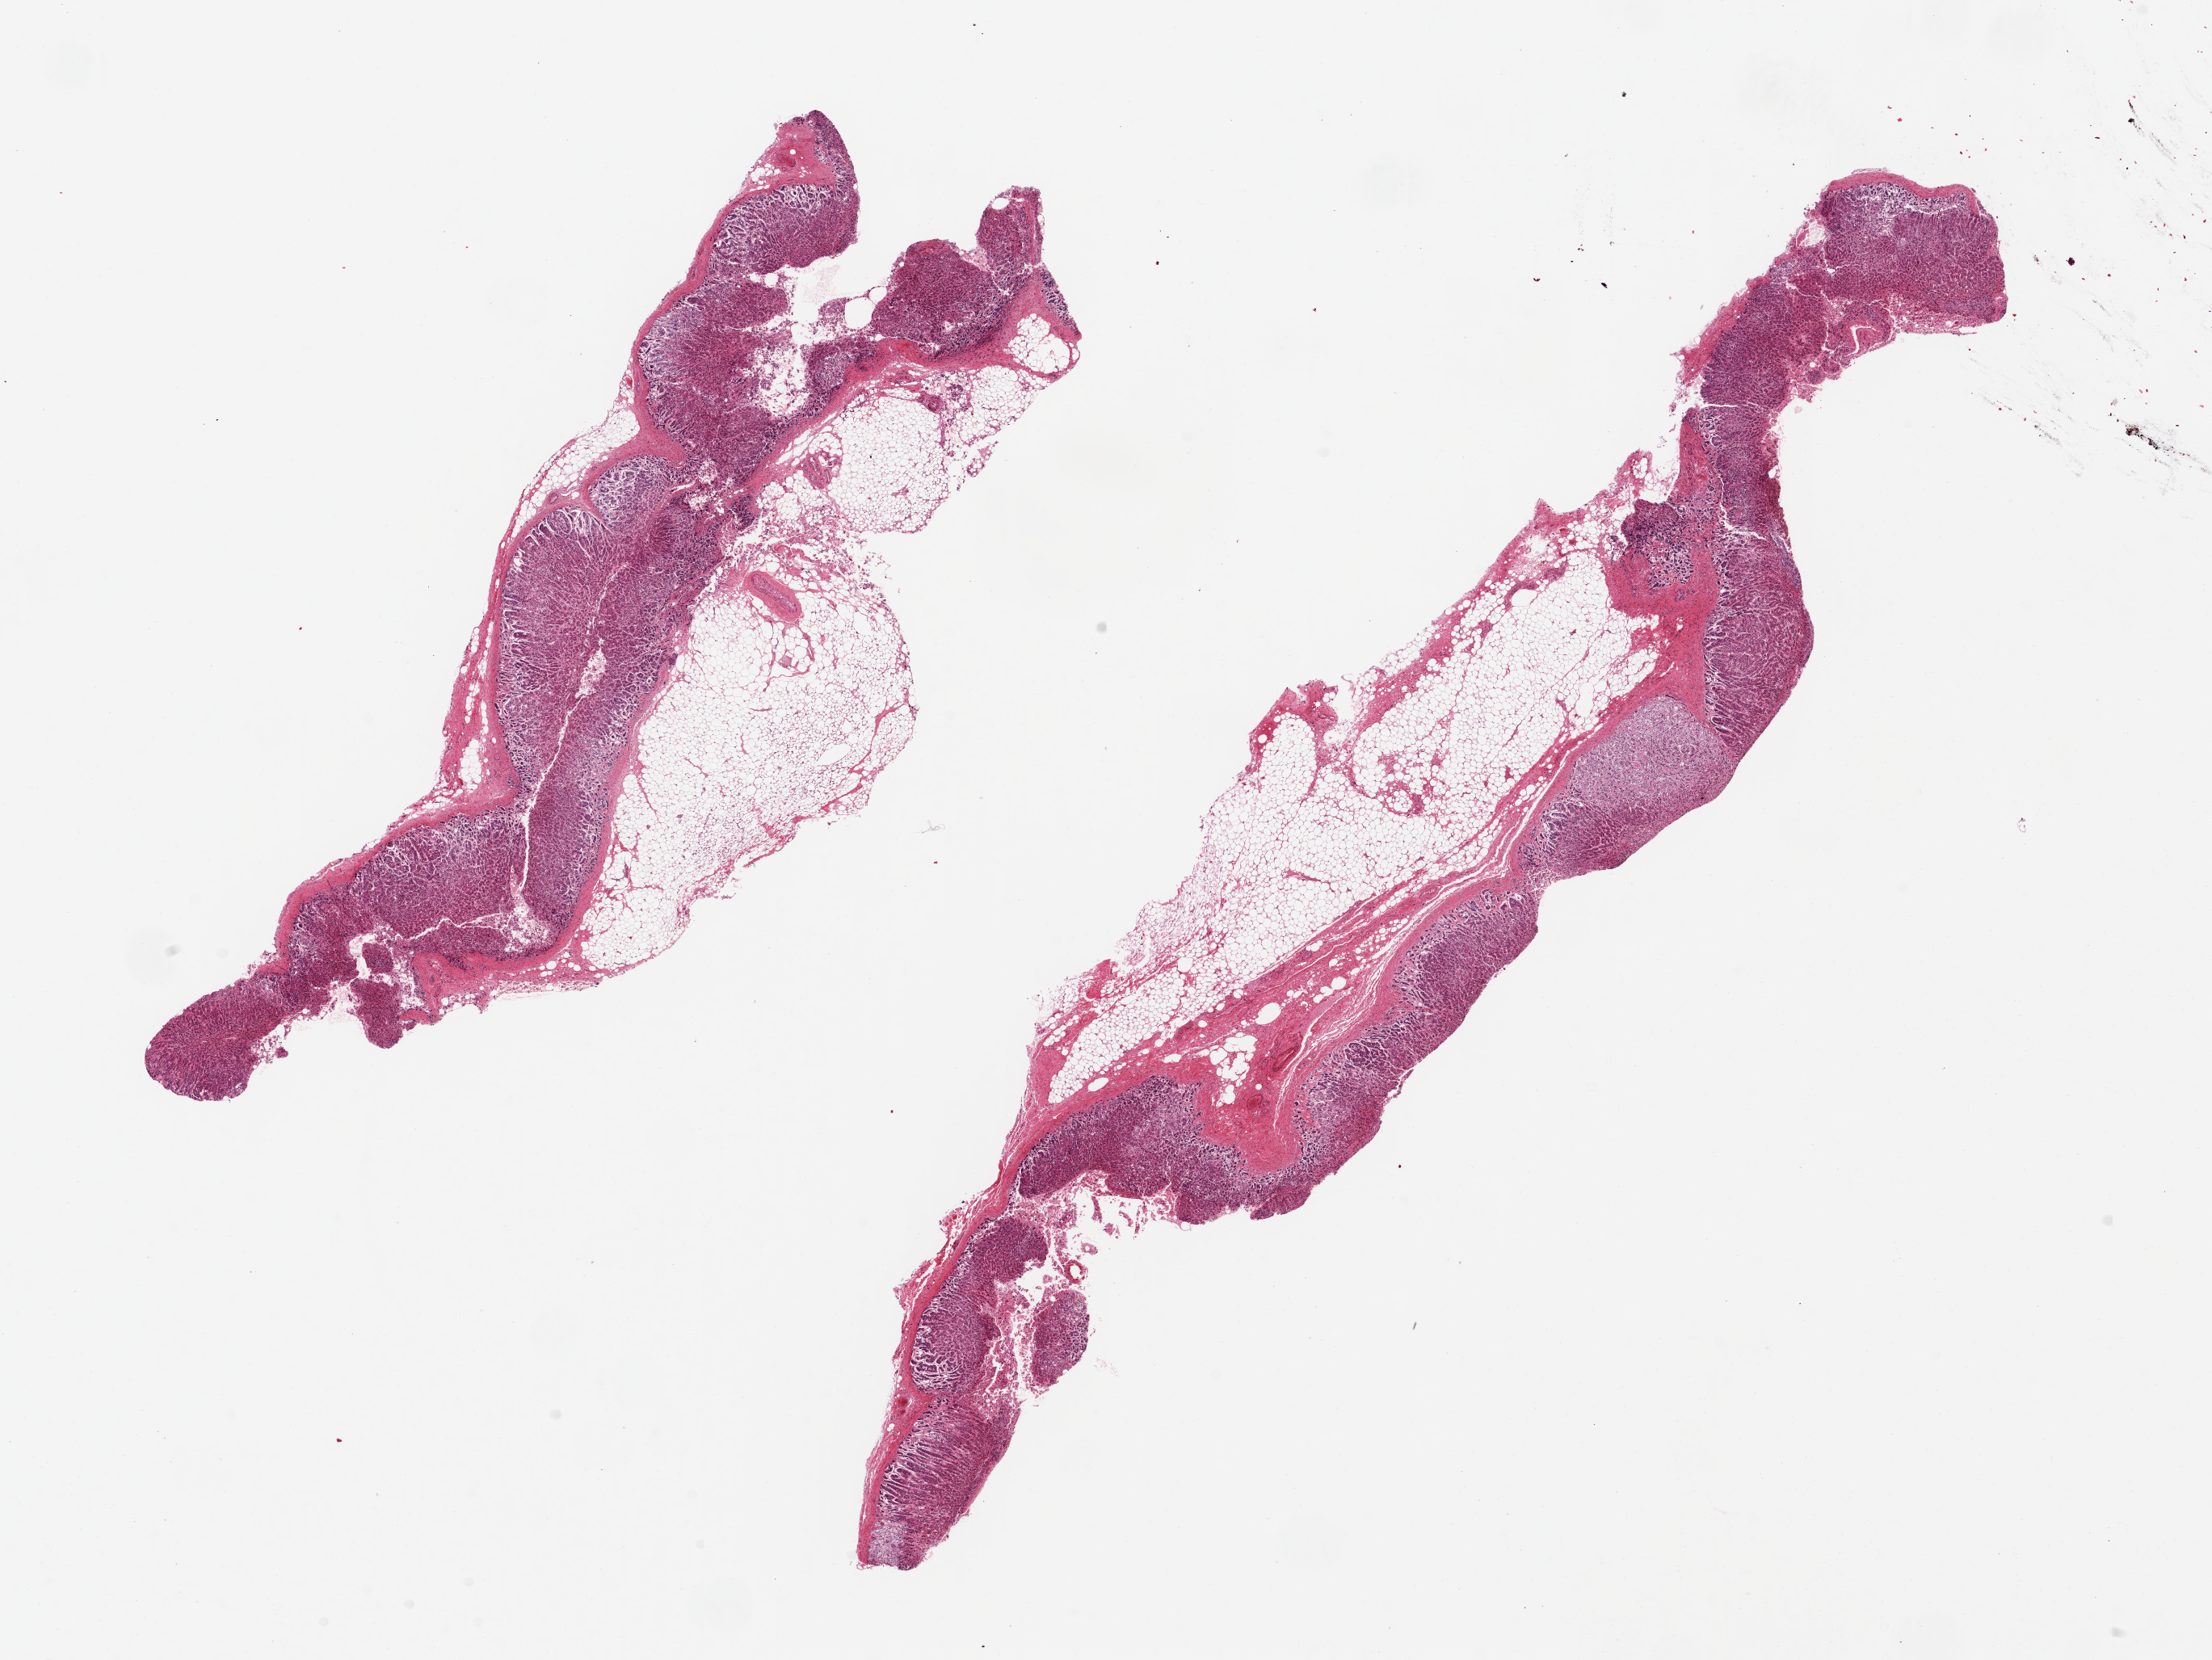
Whole-slide image, hematoxylin and eosin (H&E) stain, shown as a low-resolution overview of the whole scanned area (about 21.7 x 16.3 mm, from a 20x scan). PAXgene-fixed, paraffin-embedded tissue. Section of adrenal gland (target tissue). Donor tissue sample.
Review note (as recorded): 2 pieces ~14x2mm, all cortex, each aliquot ~40-50% fat.